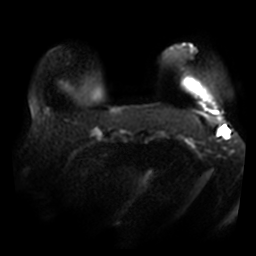
Breast MRI, one axial slice; diffusion-weighted series; image 2 of 4 stored at this slice position (different b-values; order by instance number); 3 T; 256 × 256 image matrix, field of view 400 × 400 mm. Female patient.
Outlined on this slice (manually delineated by an expert):
- tumour on diffusion-weighted imaging: bounding box [x1, y1, x2, y2] px = [225, 129, 229, 135]